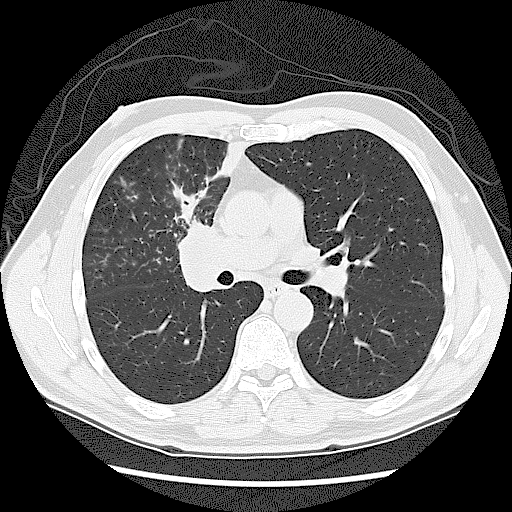
Low-dose screening chest CT, axial slice. First (baseline) screen. Lung window (W 1500 / L -600 HU). 2.5 mm slice thickness. 512 × 512 image matrix. Male, age 60 years at enrolment.
• Expert-annotated lung lesion, box from (x=158, y=216) to (x=241, y=307) px.
• No non-calcified nodule or mass ≥4 mm was recorded by the screening reader at this exam.
• Participant outcome: lung cancer diagnosed 41 days after this screen — small cell carcinoma, NOS, right upper lobe, stage IIIA (AJCC 6th edition).